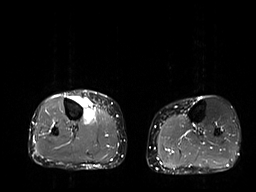
MRI of an extremity soft-tissue mass, one axial slice. Position 15 of 32 along the scan axis. STIR. 6 mm slice thickness. 256 × 192 image matrix, field of view 375 × 281 mm. Female patient. From the clinical record (not read from this slice): histological type: undifferentiated – high grade; grade: high; site of the primary tumour: right thigh.
Outlined on this slice (outlined manually by an expert reader):
- gross tumour volume (mass): bounding box <70,95,95,125> (left, top, right, bottom; pixels)